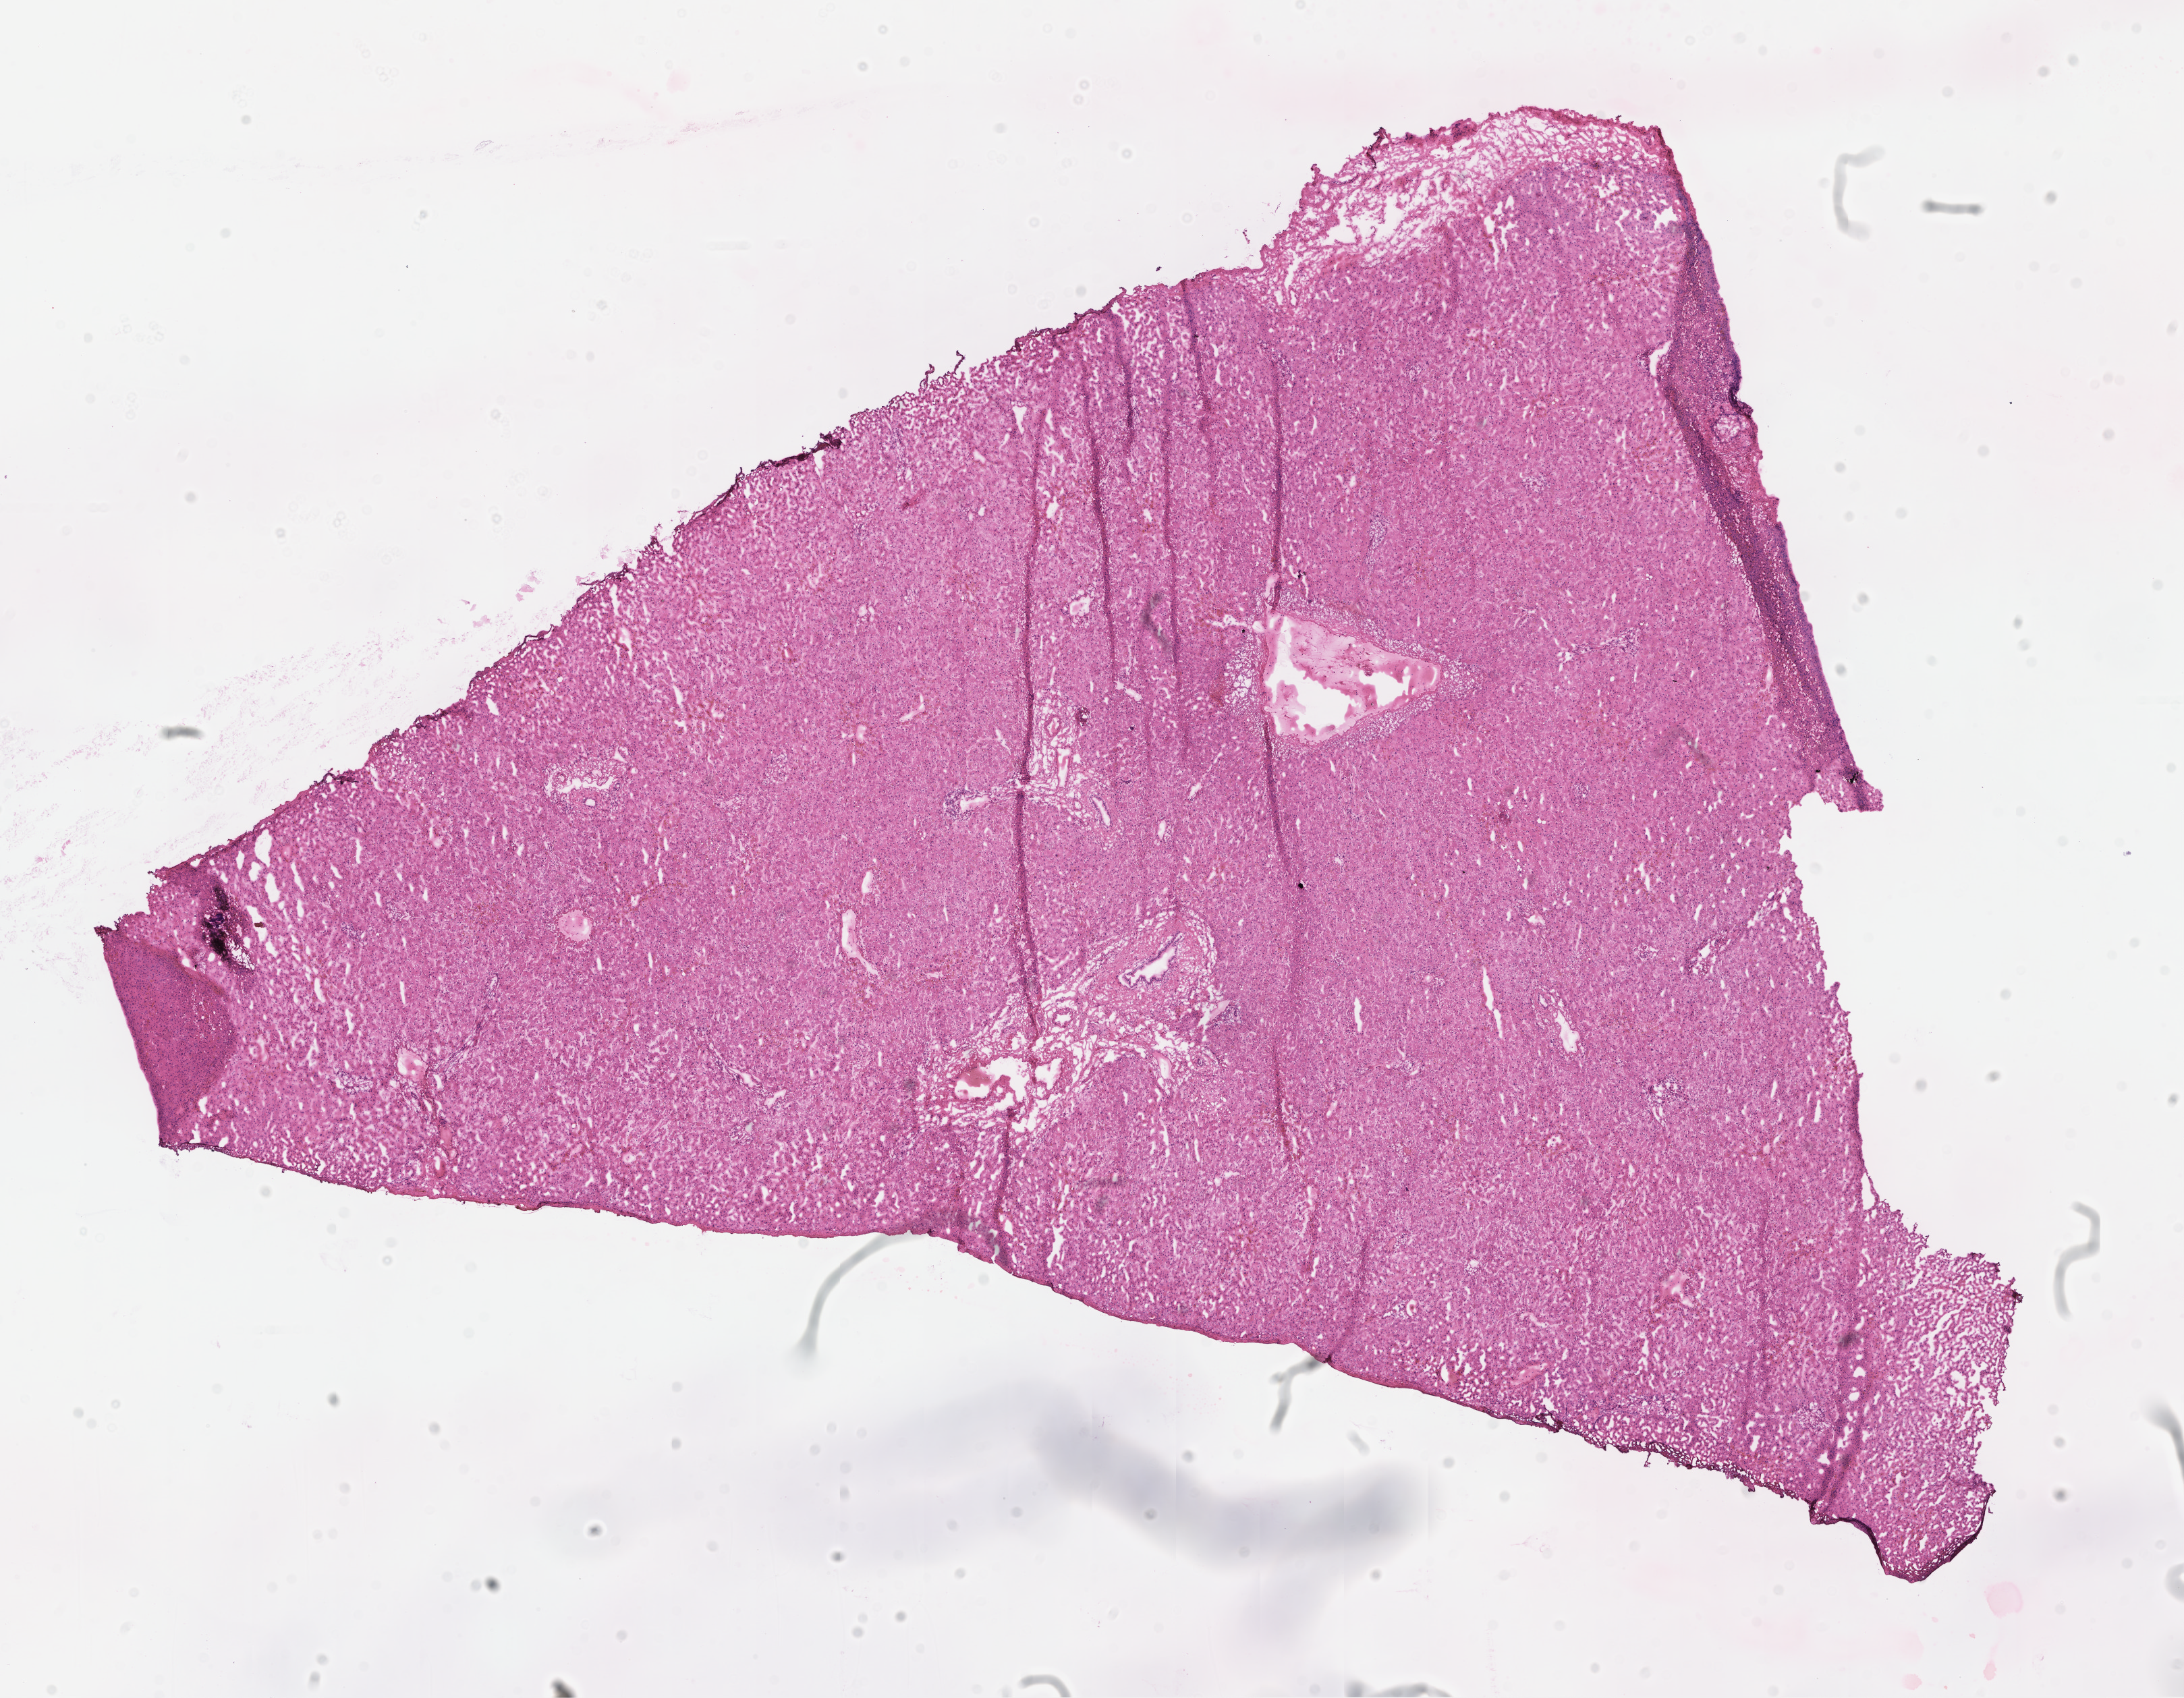
Haematoxylin and eosin whole-slide image — a low-resolution overview of the entire scanned area, about 13.1 x 10.2 mm. Cryosection. Specimen: normal-tissue sample (non-tumor) from a patient with adenocarcinoma, NOS. Site: rectosigmoid junction. Patient: male, age at initial diagnosis 65 years. Slide review estimates, as recorded: tumor cells 0%, tumor nuclei 0%, stromal cells 0%, necrosis 0%, normal cells 100%. Inflammatory infiltration, as recorded: lymphocyte infiltration 0%, monocyte infiltration 0%, neutrophil infiltration 0%.
* this section: non-tumor tissue sample; the patient's diagnosis is given above
* section: bottom of the tissue portion